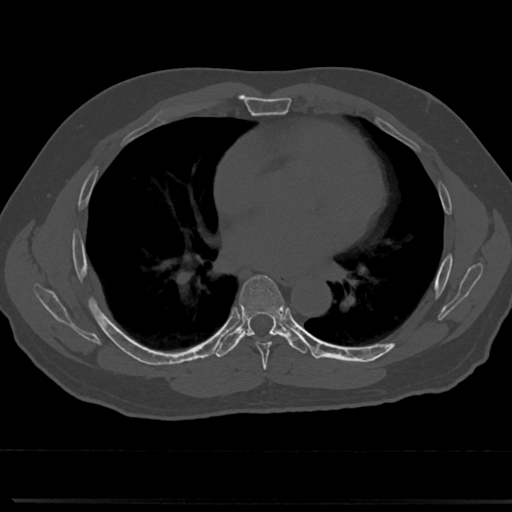
CT including the spine, one axial slice; slice 423 of 817 in the series (ordered by position); reconstruction kernel Br40s/3; bone window (W 1800 / L 400 HU); 512 × 512 image matrix, field of view 355 × 355 mm. Male patient, age 61 years. Case-level facts recorded for this patient, not image findings: primary cancer: prostate.
Annotated regions visible in this slice (semi-automatically segmented with operator editing):
- T6 vertebra: bounding box (x1, y1, x2, y2) in pixels: (240, 275, 287, 360)
- T7 vertebra: (239, 315, 286, 335)